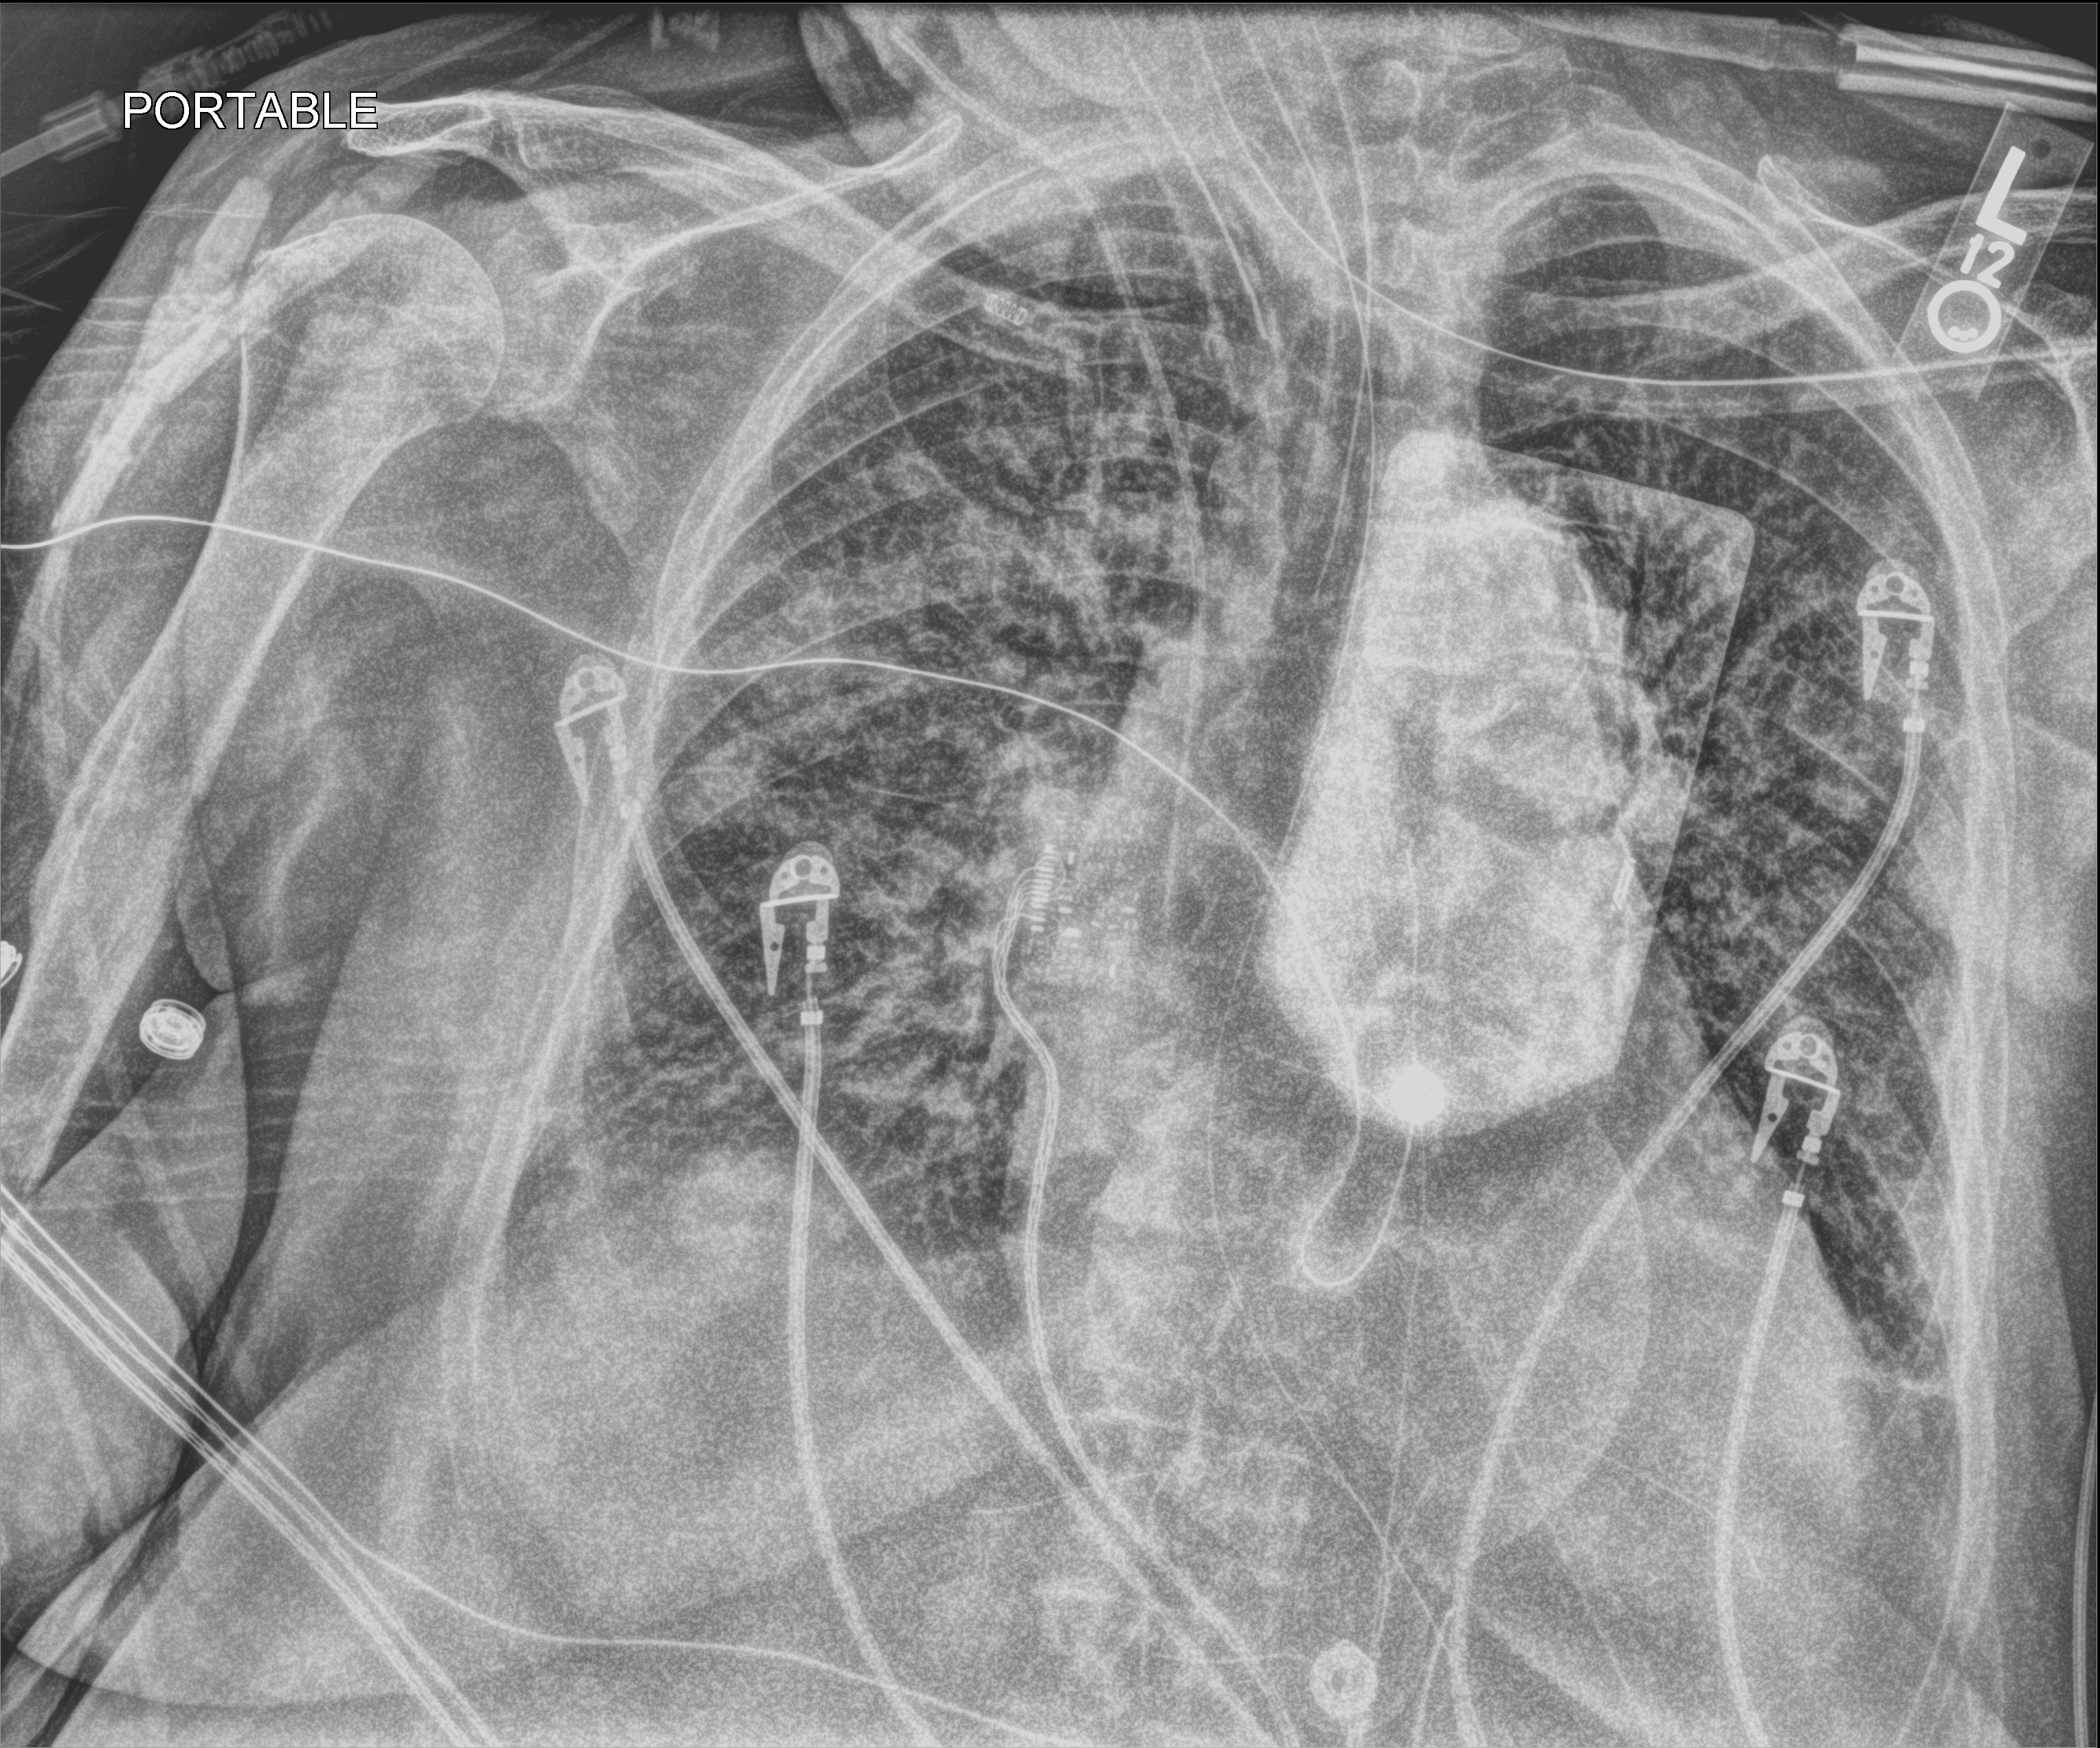
Portable chest radiograph. Patient hospitalised with COVID-19; female, aged 75–90 years.
From the hospital-stay record, not from the radiograph (when in the stay this image was taken is not recorded):
- mechanically ventilated during this hospital stay: yes
- admitted to intensive care during this hospital stay: yes